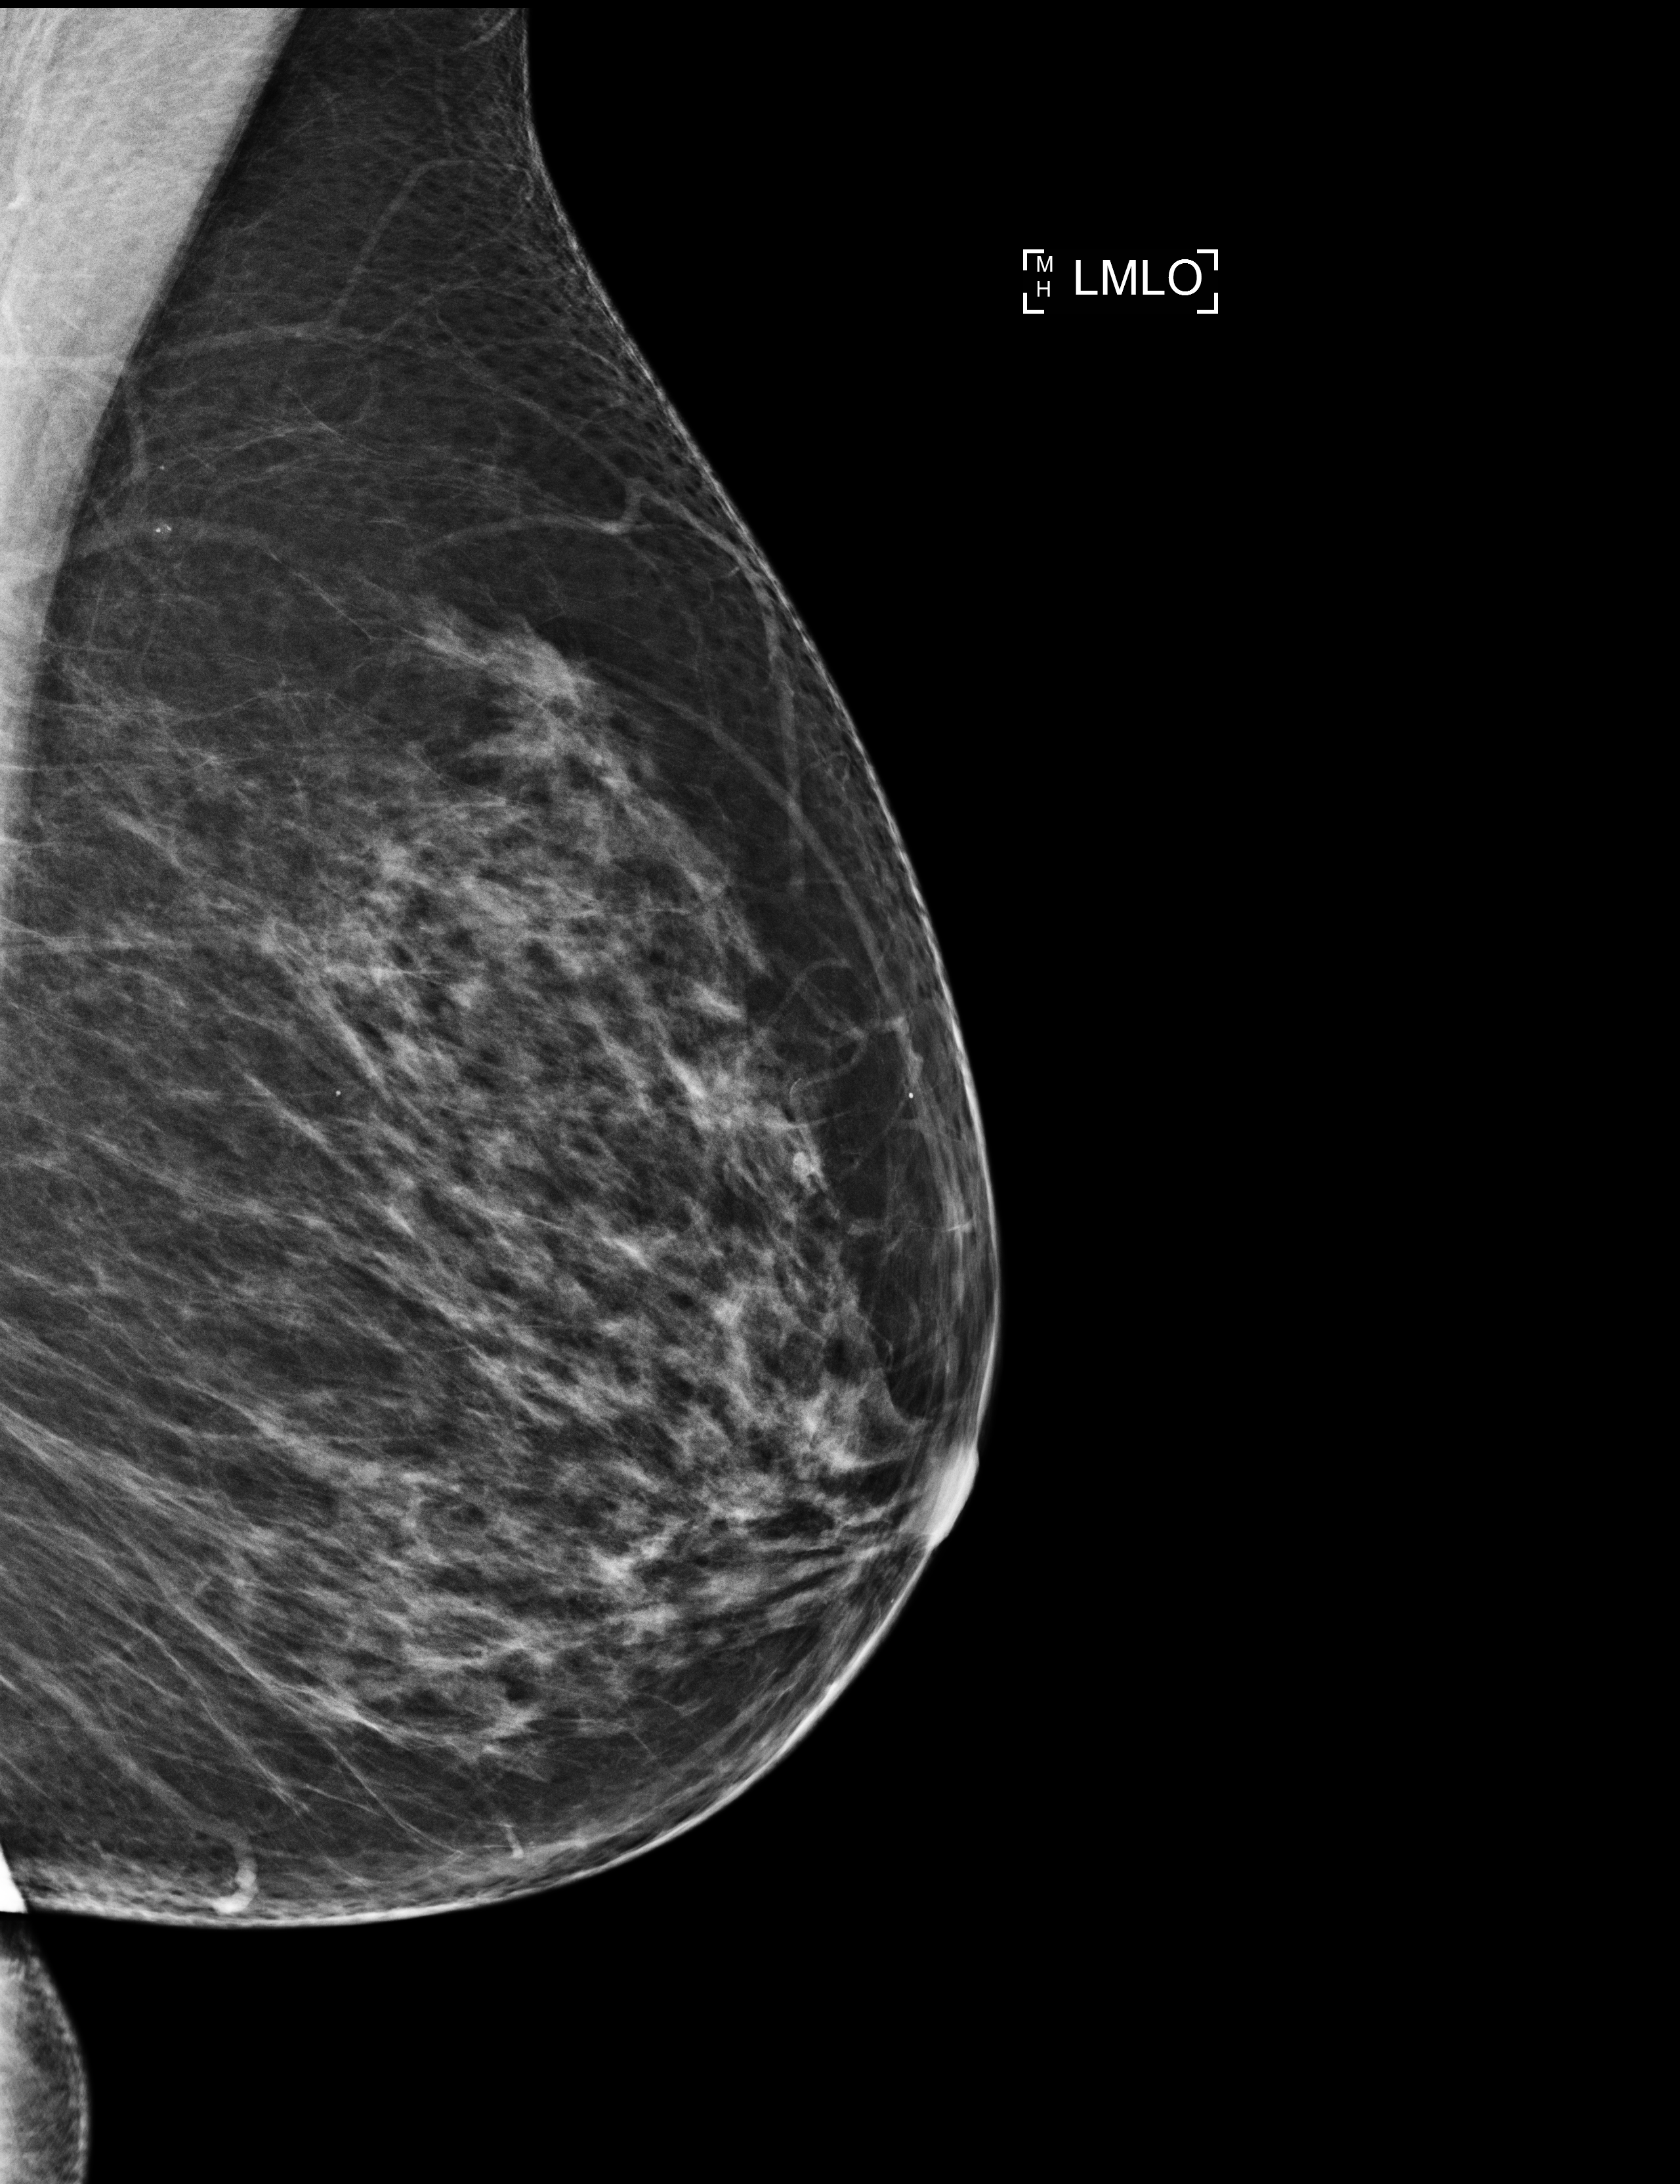
Annual screening mammography examination. Female patient, age 71 years.
Image type: full-field digital mammogram. Breast: left. Projection: medio-lateral oblique projection.